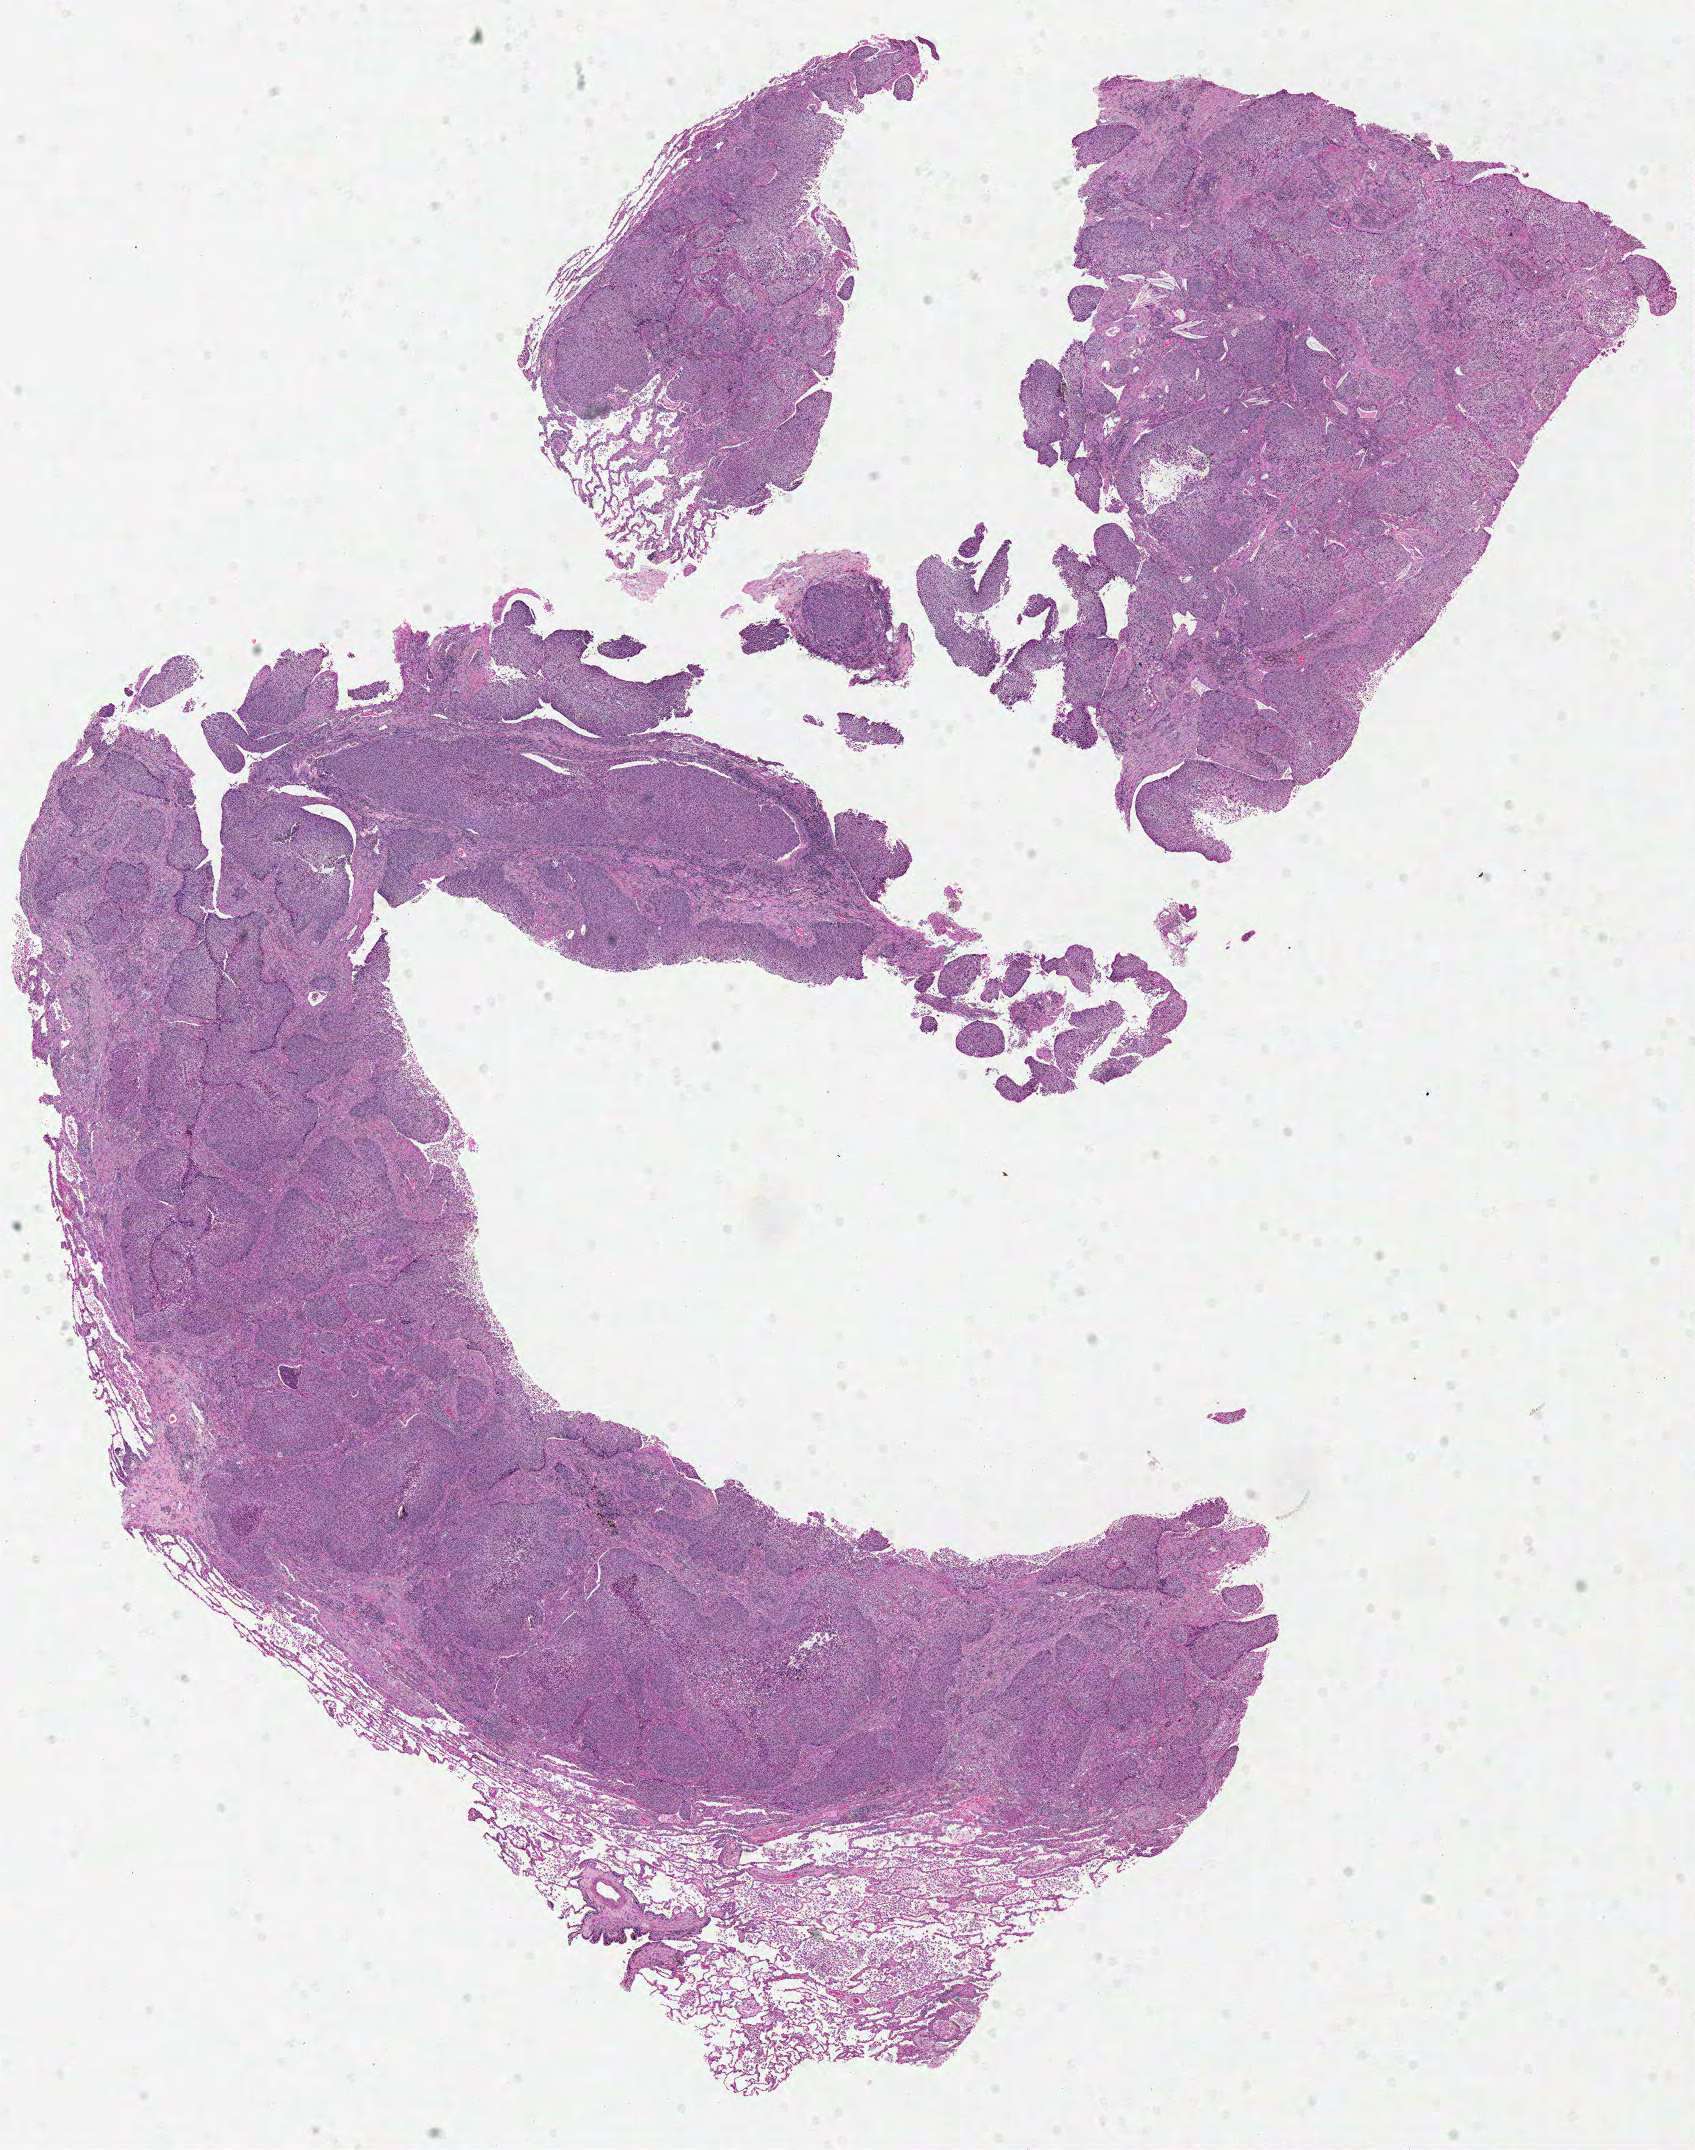
Digitized Hematoxylin and eosin (H&E) stained tissue section (whole slide), low-resolution overview of the scanned area, about 13.4 x 16.9 mm (slide scanned at 40x). Formalin-fixed paraffin-embedded (FFPE) diagnostic section. Lung, primary tumour sample. Patient: male, age at initial diagnosis 70 years.
TNM: T2 N1 M1. Histologic diagnosis: Squamous cell carcinoma, NOS (upper lobe, lung). Laterality: right. AJCC pathologic stage: IV (5th edition).